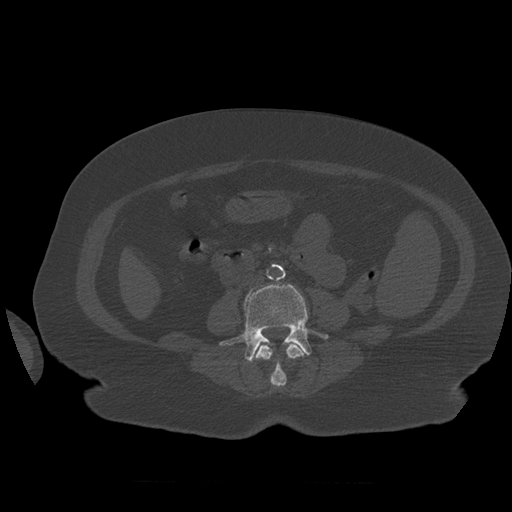
CT including the spine, one axial slice; slice 214 of 399 in the series (ordered by position); reconstruction kernel STANDARD; 120 kVp; bone window (W 1800 / L 400 HU); 512 × 512 image matrix, field of view 404 × 404 mm. Patient age 81 years. From the clinical record (not read from this slice): primary cancer: renal; vertebrae with lytic lesions (as recorded): L1.
Structures marked on this image (semi-automatically segmented with operator editing):
- L3 vertebra: bounding box [x1, y1, x2, y2] px = [255, 343, 307, 387]
- L4 vertebra: [220, 283, 329, 362]